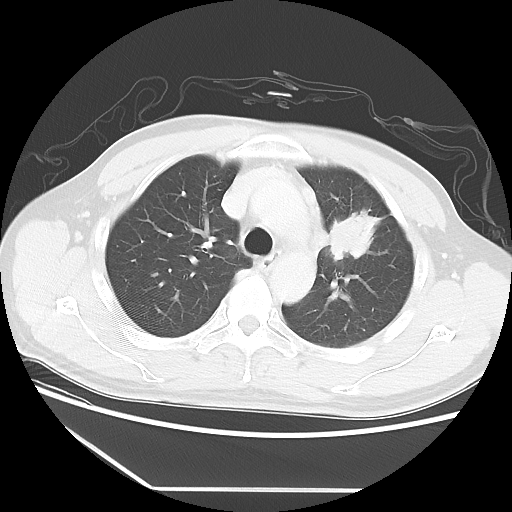
Chest CT, one axial slice. Slice 40 of 56 in the series (ordered by position). 120 kVp. Lung window (W 1500 / L -600 HU). 512 × 512 image matrix. Male patient, age 53 years. From the clinical record (not read from this slice): clinical TNM (as recorded): T2a N1 M1b.
Structures marked on this image (bounding box drawn by a radiologist):
- lung tumour (recorded histology: adenocarcinoma): box from (x=331, y=203) to (x=386, y=268) px